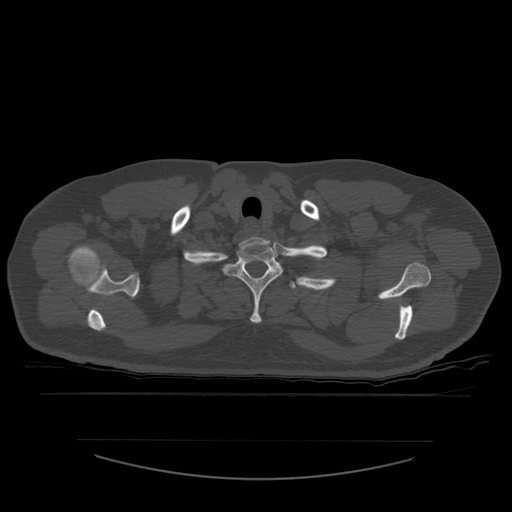
CT including the spine, one axial slice; position 468 of 532 along the scan axis; 120 kVp; bone window (W 1800 / L 400 HU); 1.25 mm slice thickness; 512 × 512 image matrix, field of view 441 × 441 mm. Patient age 44 years. Case-level facts recorded for this patient, not image findings: primary cancer: soft tissue sarcoma.
Annotated regions visible in this slice (semi-automatic segmentation, software-assisted and operator-edited):
- T1 vertebra: box from (x=223, y=245) to (x=283, y=324) px
- T2 vertebra: (x=290, y=280)–(x=313, y=290)